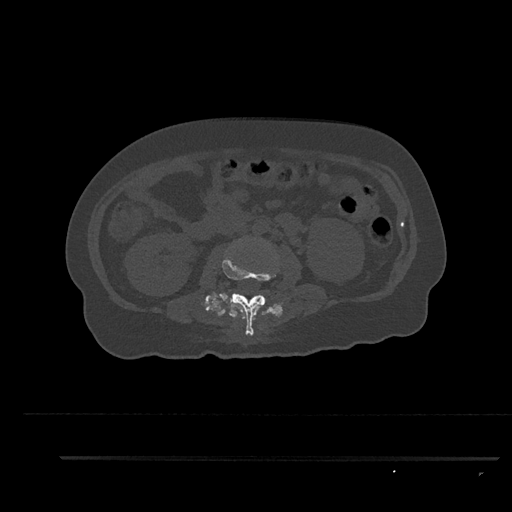
CT including the spine, one axial slice. Slice 134 of 797 in the series (ordered by position). Bone window (W 1800 / L 400 HU). 0.5 mm slice thickness. 512 × 512 image matrix. Female patient, age 44 years. From the clinical record (not read from this slice): primary cancer: renal; vertebrae with lytic lesions (as recorded): L1.
Outlined on this slice (semi-automatic segmentation, software-assisted and operator-edited):
- L2 vertebra: bounding box <222,253,276,336> (left, top, right, bottom; pixels)